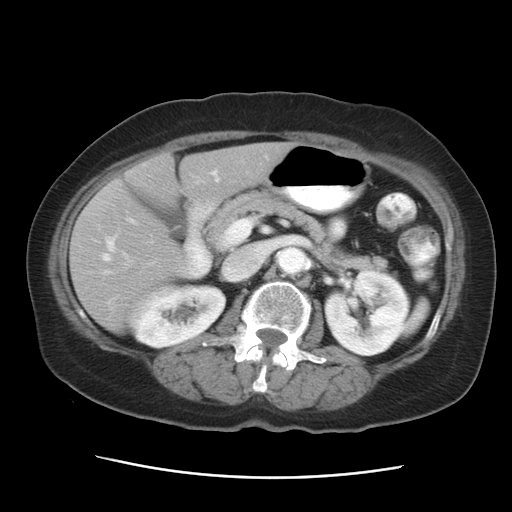
Contrast-enhanced abdominal CT, one axial slice. Slice 14 of 29 in the series (ordered by position). Reconstruction kernel STANDARD. 120 kVp. Intravenous contrast given. Soft-tissue window (W 400 / L 40 HU). 7.5 mm slice thickness. 512 × 512 image matrix, field of view 354 × 354 mm. Female patient, age 64 years. Case-level facts recorded for this patient, not image findings: diagnosis: colorectal cancer liver metastases, imaged before liver resection; multiple liver metastases: no; largest metastasis: 2.5 cm; disease in both lobes: no.
Annotated regions visible in this slice (outlined manually by an expert reader):
- hepatic veins: bounding box (x1, y1, x2, y2) in pixels: (102, 172, 216, 261)
- liver: (71, 143, 293, 331)
- planned liver remnant (the part of the liver to remain after resection): (71, 143, 293, 329)
- portal vein (with intrahepatic branches): (129, 219, 237, 247)